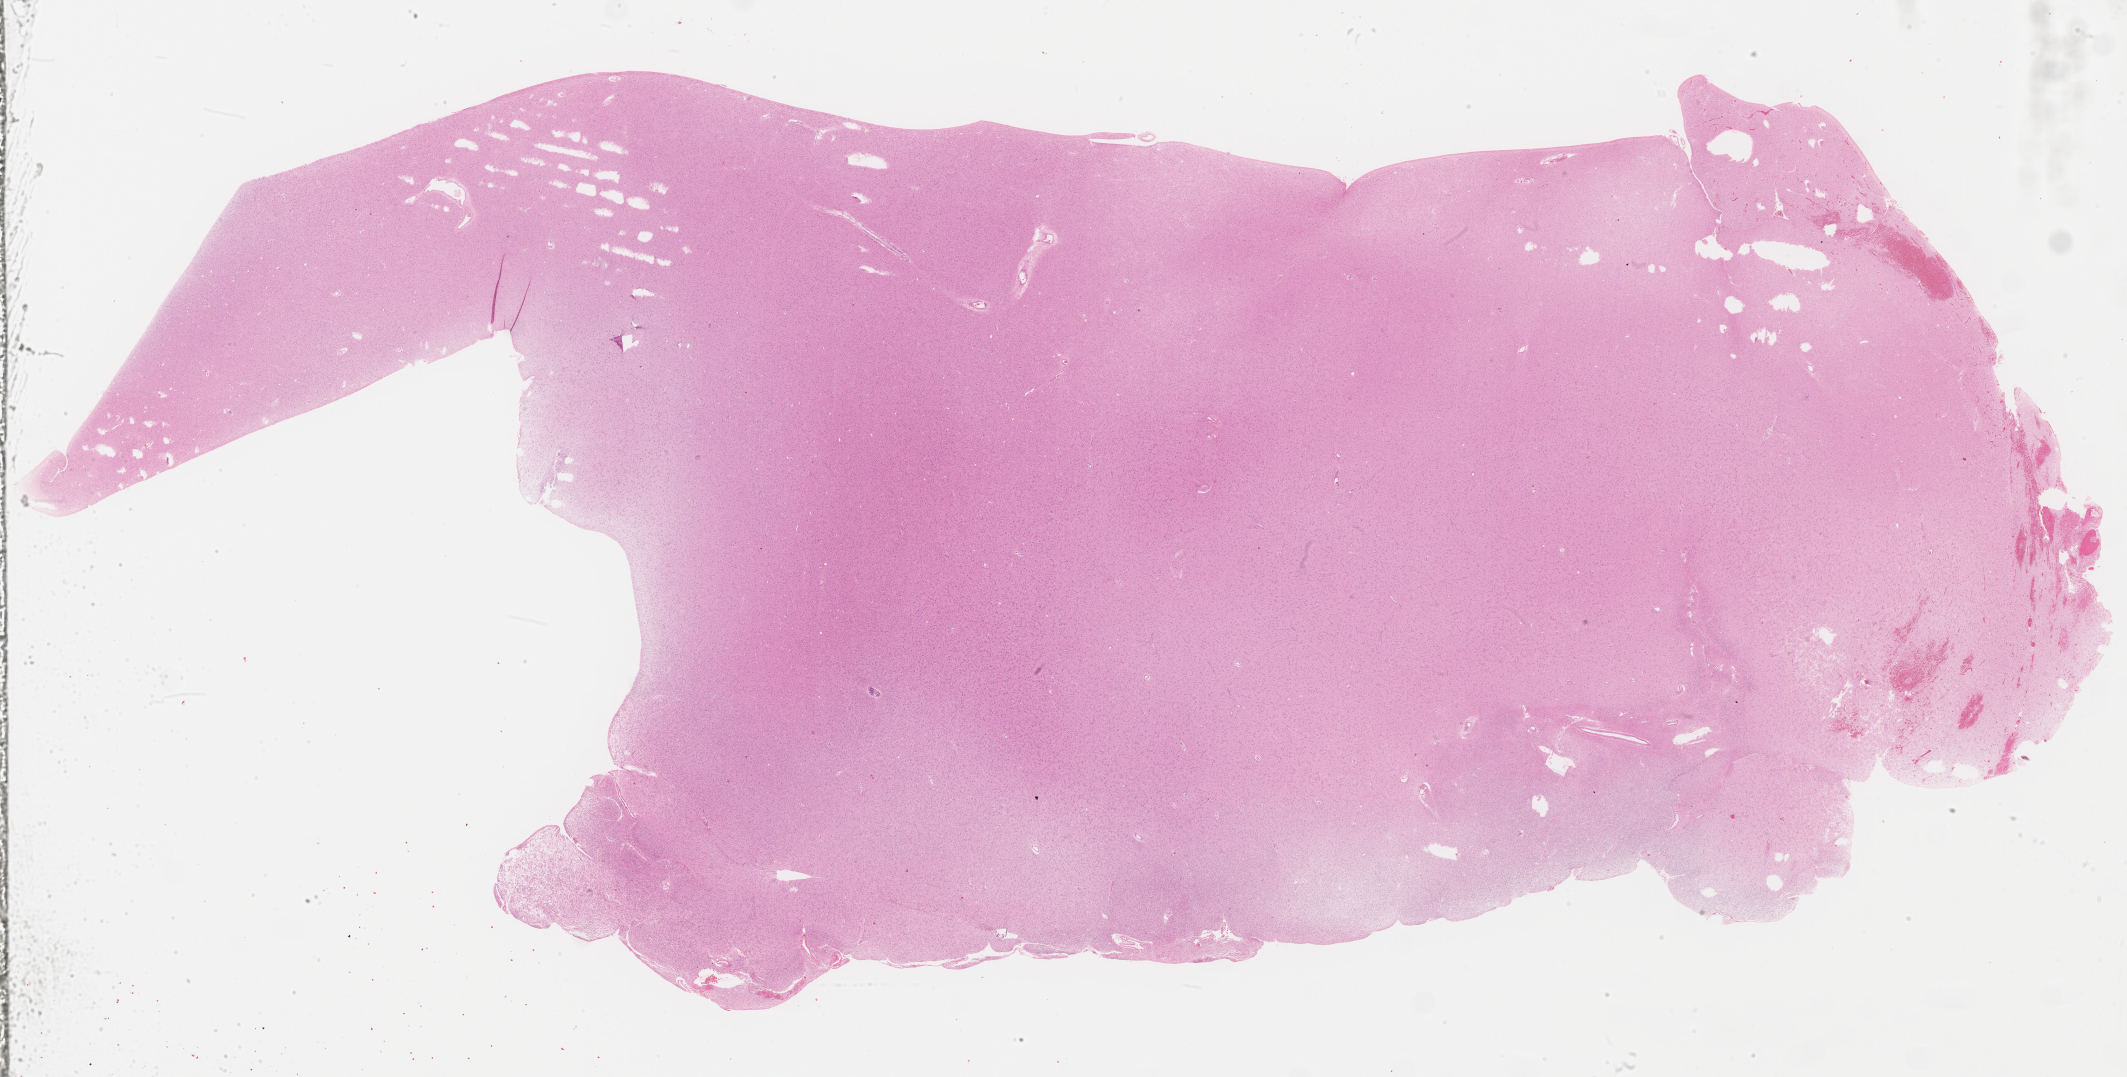
Digitized H&E tissue section (whole slide), shown as a low-resolution overview of the whole scanned area (about 34.3 x 17.4 mm, from a 40x scan); formalin-fixed paraffin-embedded (FFPE) diagnostic section; sample: primary tumour, brain. Patient: male, age at initial diagnosis 40 years. Histologic grade: G2 (moderately differentiated).
Diagnosis: Oligodendroglioma, NOS. Laterality: right.